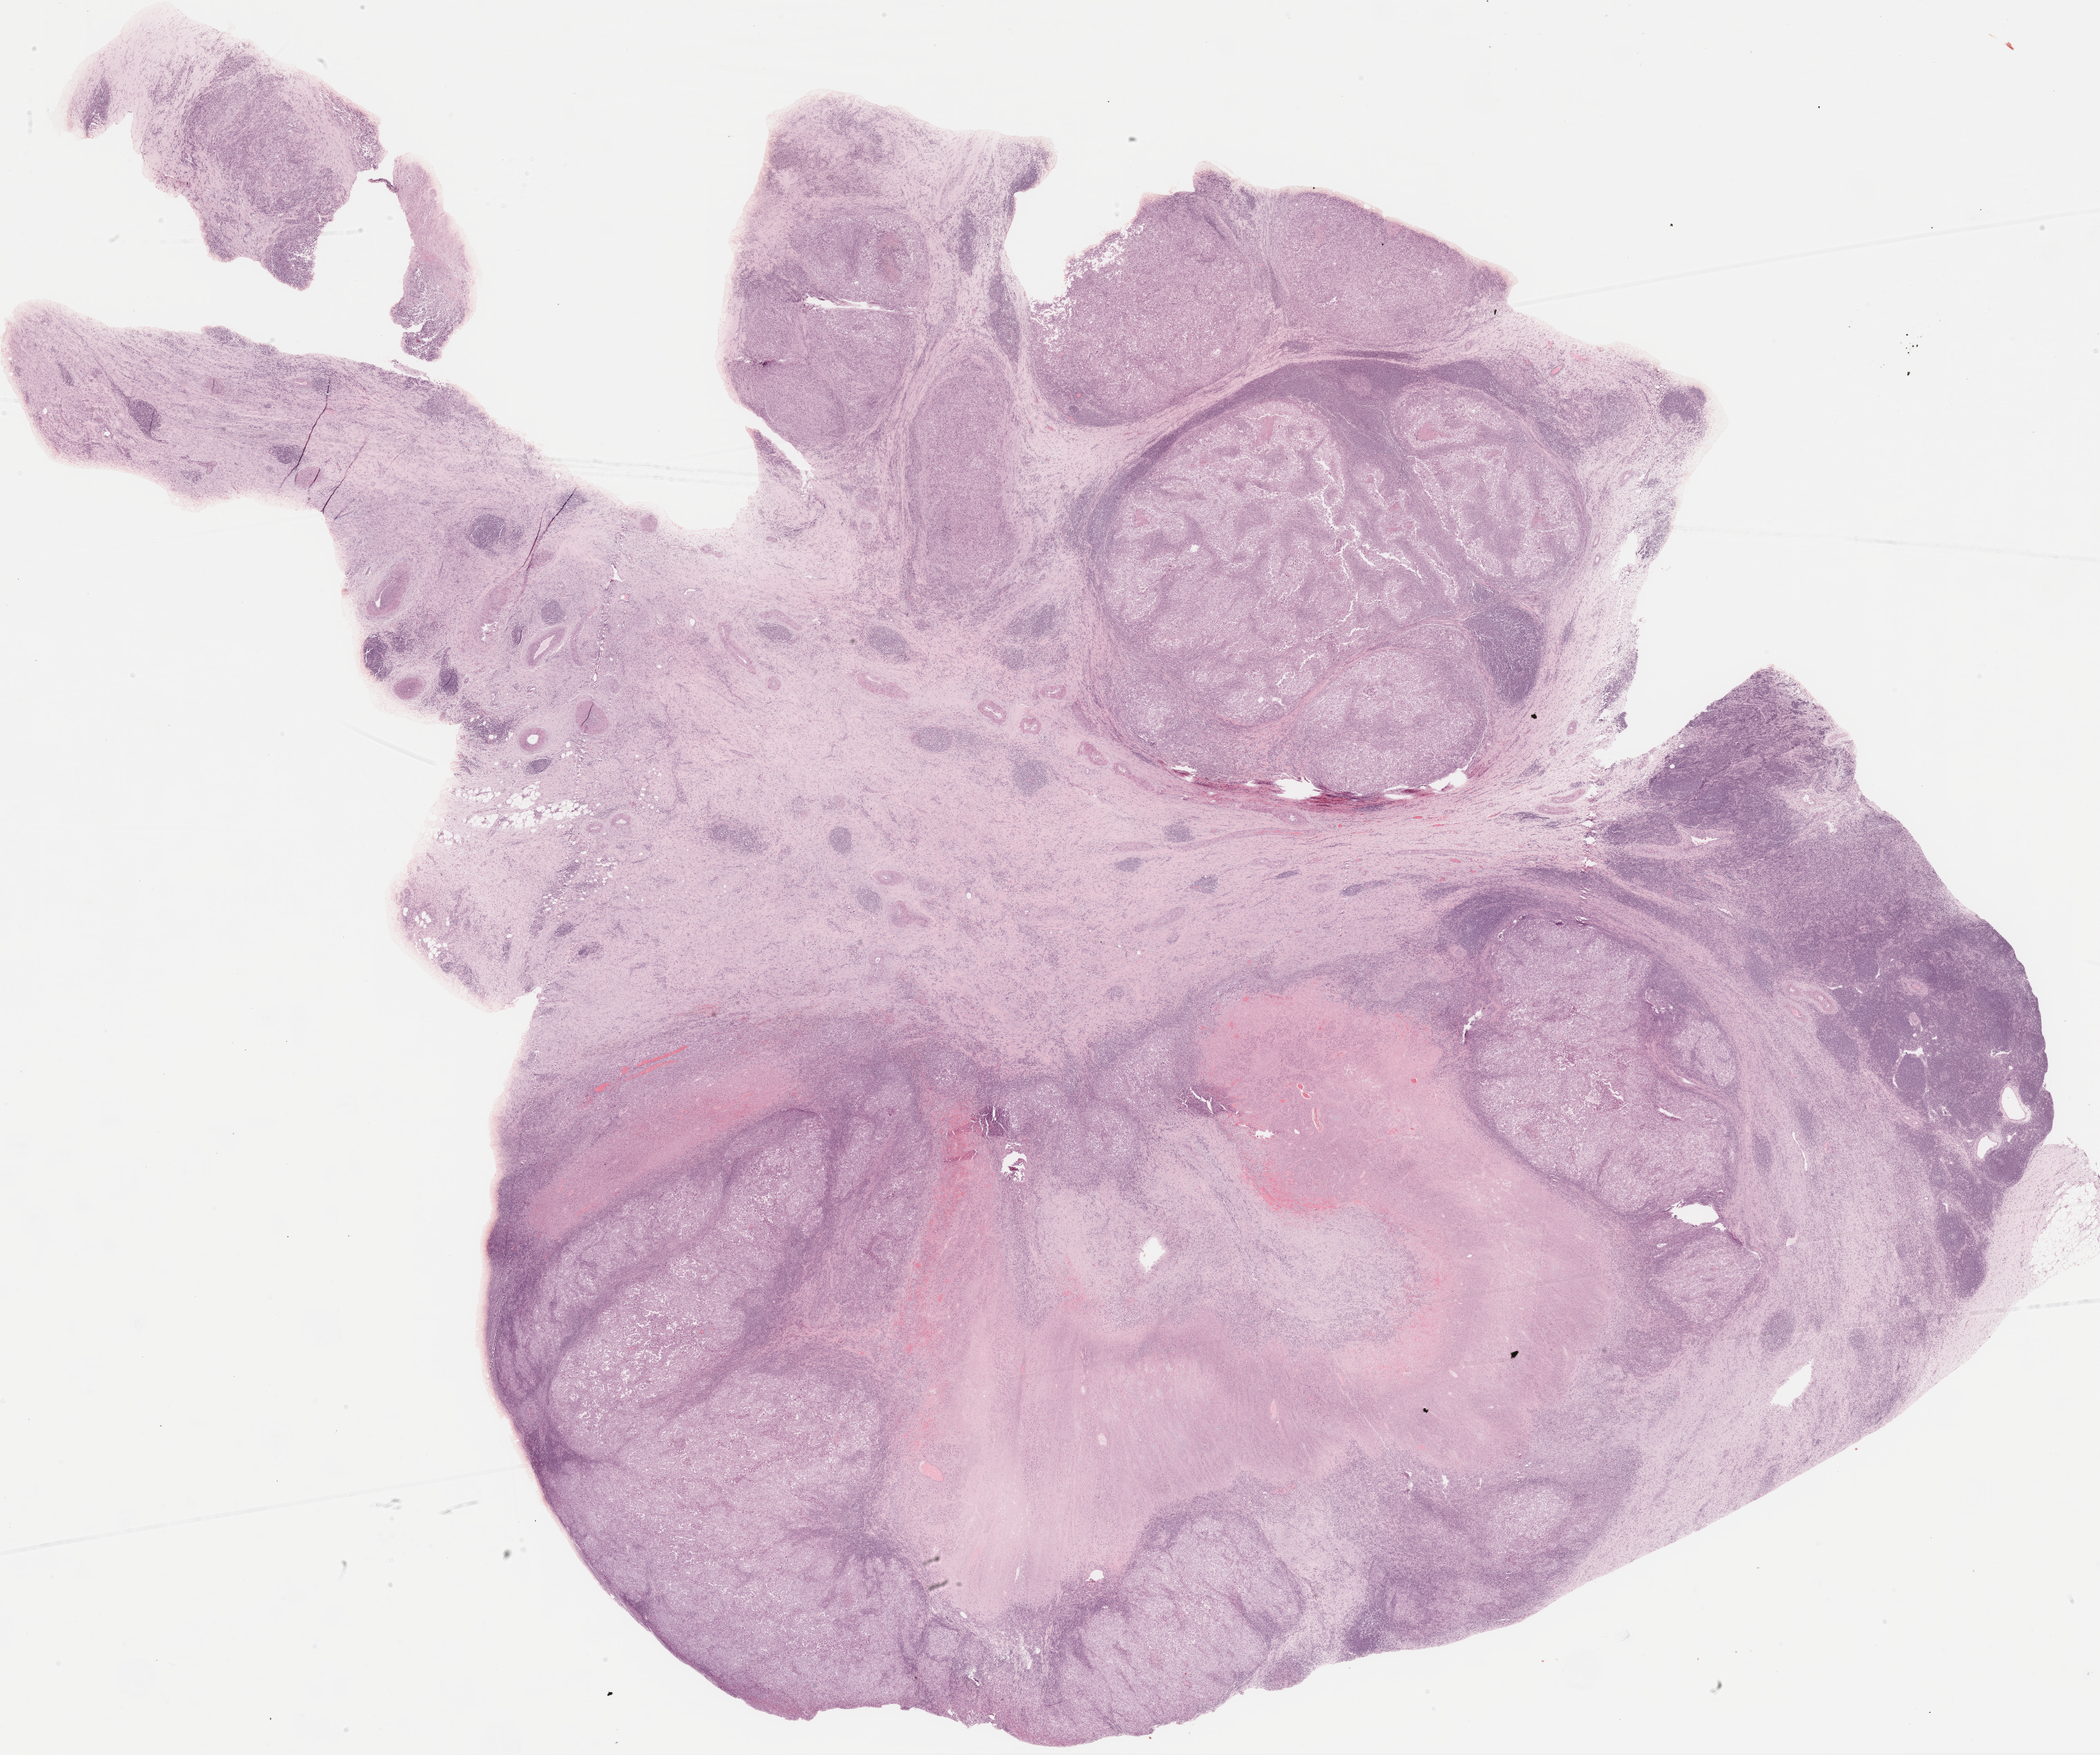
Whole-slide histology image, H&E-stained — low-resolution overview of the scanned area, about 24.5 x 20.5 mm (slide scanned at 20x); FFPE section; metastatic tumour sample, sampled site: lymph nodes of axilla or arm. Female patient; age at initial diagnosis 53 years.
This section: metastatic tumour tissue. Patient diagnosis: Malignant melanoma, NOS.